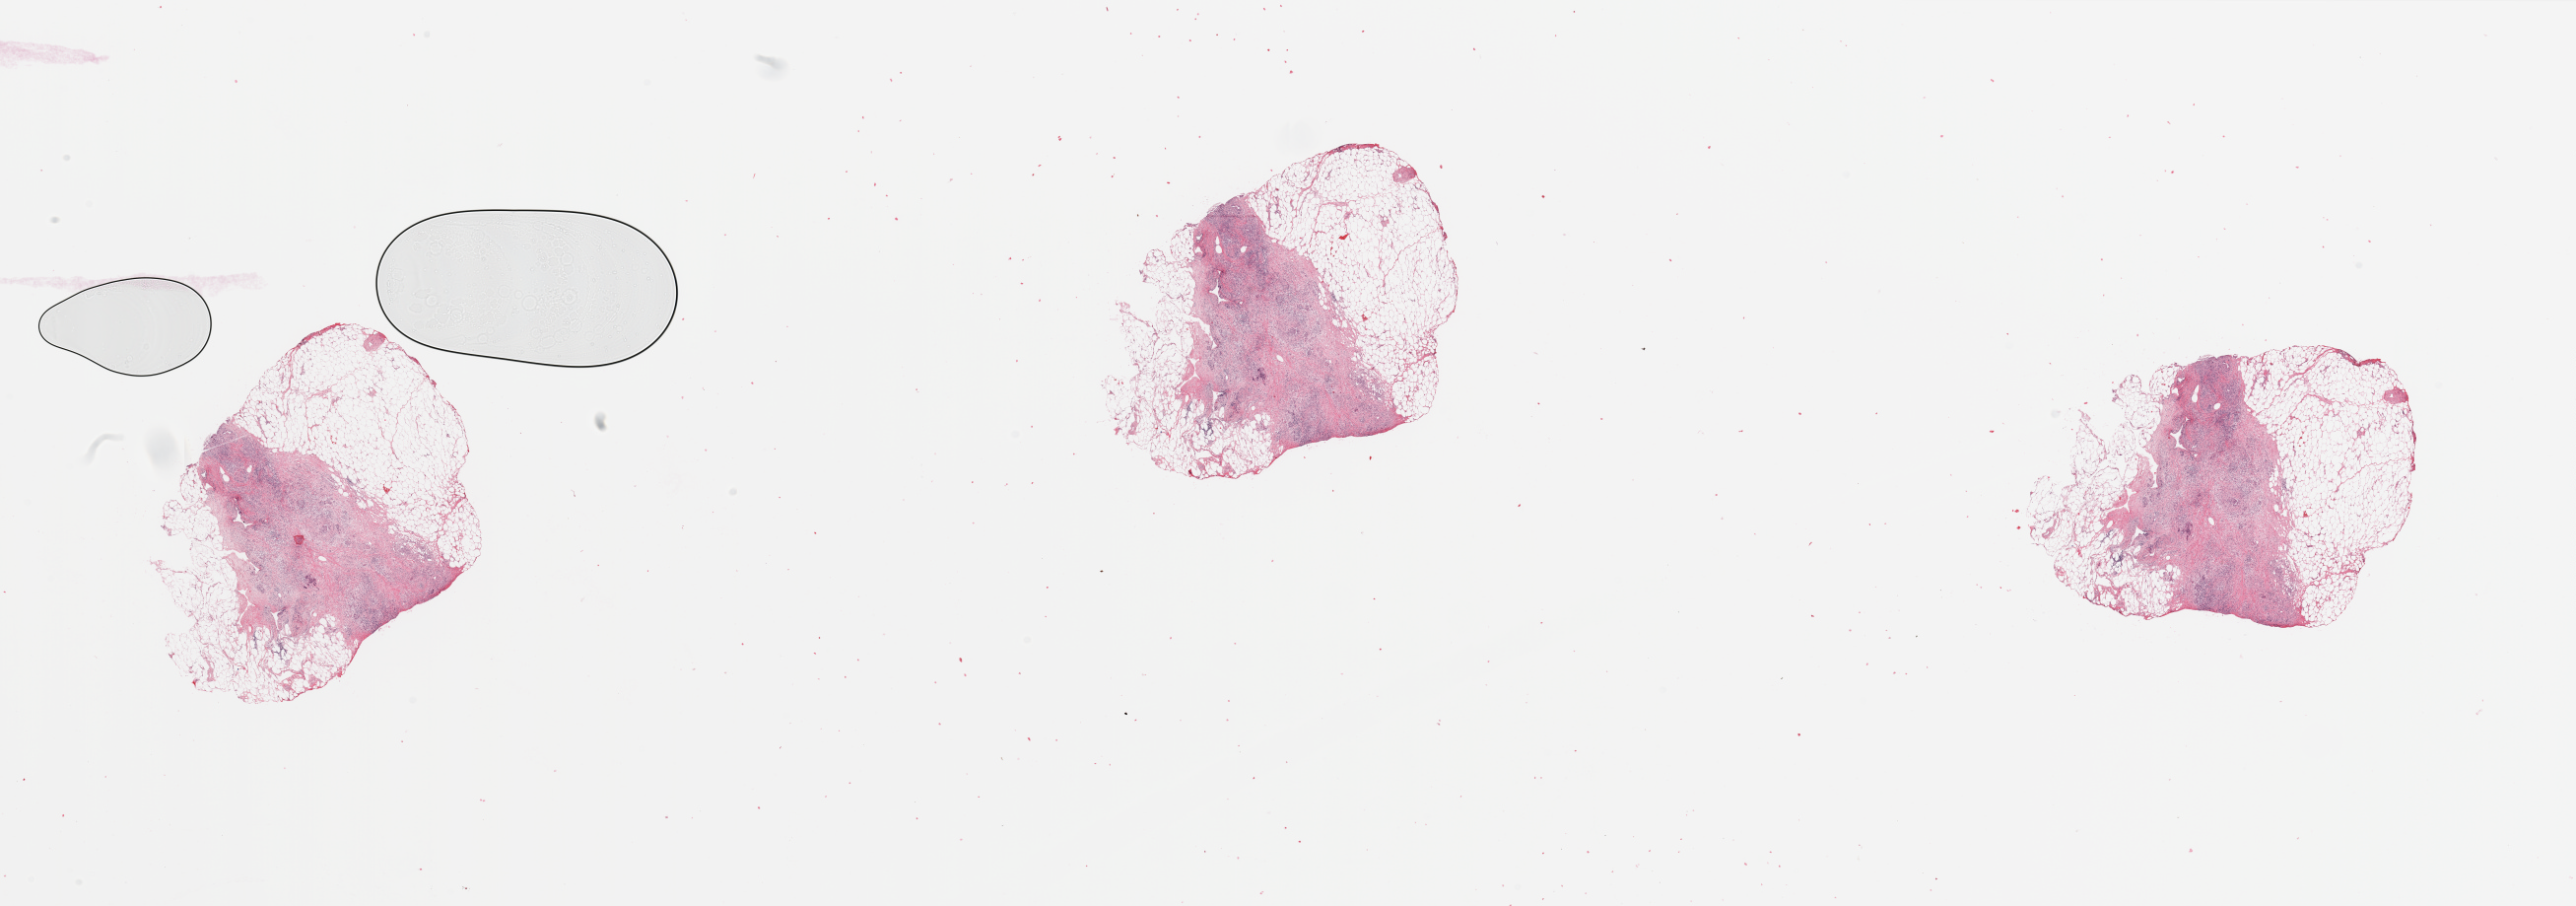
Hematoxylin and eosin (H&E) stained whole-slide image, whole scanned area (about 41.3 x 14.5 mm) shown as a low-resolution overview, tumour tissue sample, pancreas. Patient: male, age 84 years.
Patient diagnosis (cohort enrolment): ductal adenocarcinoma (pancreas). Primary tumour site (as recorded): head.